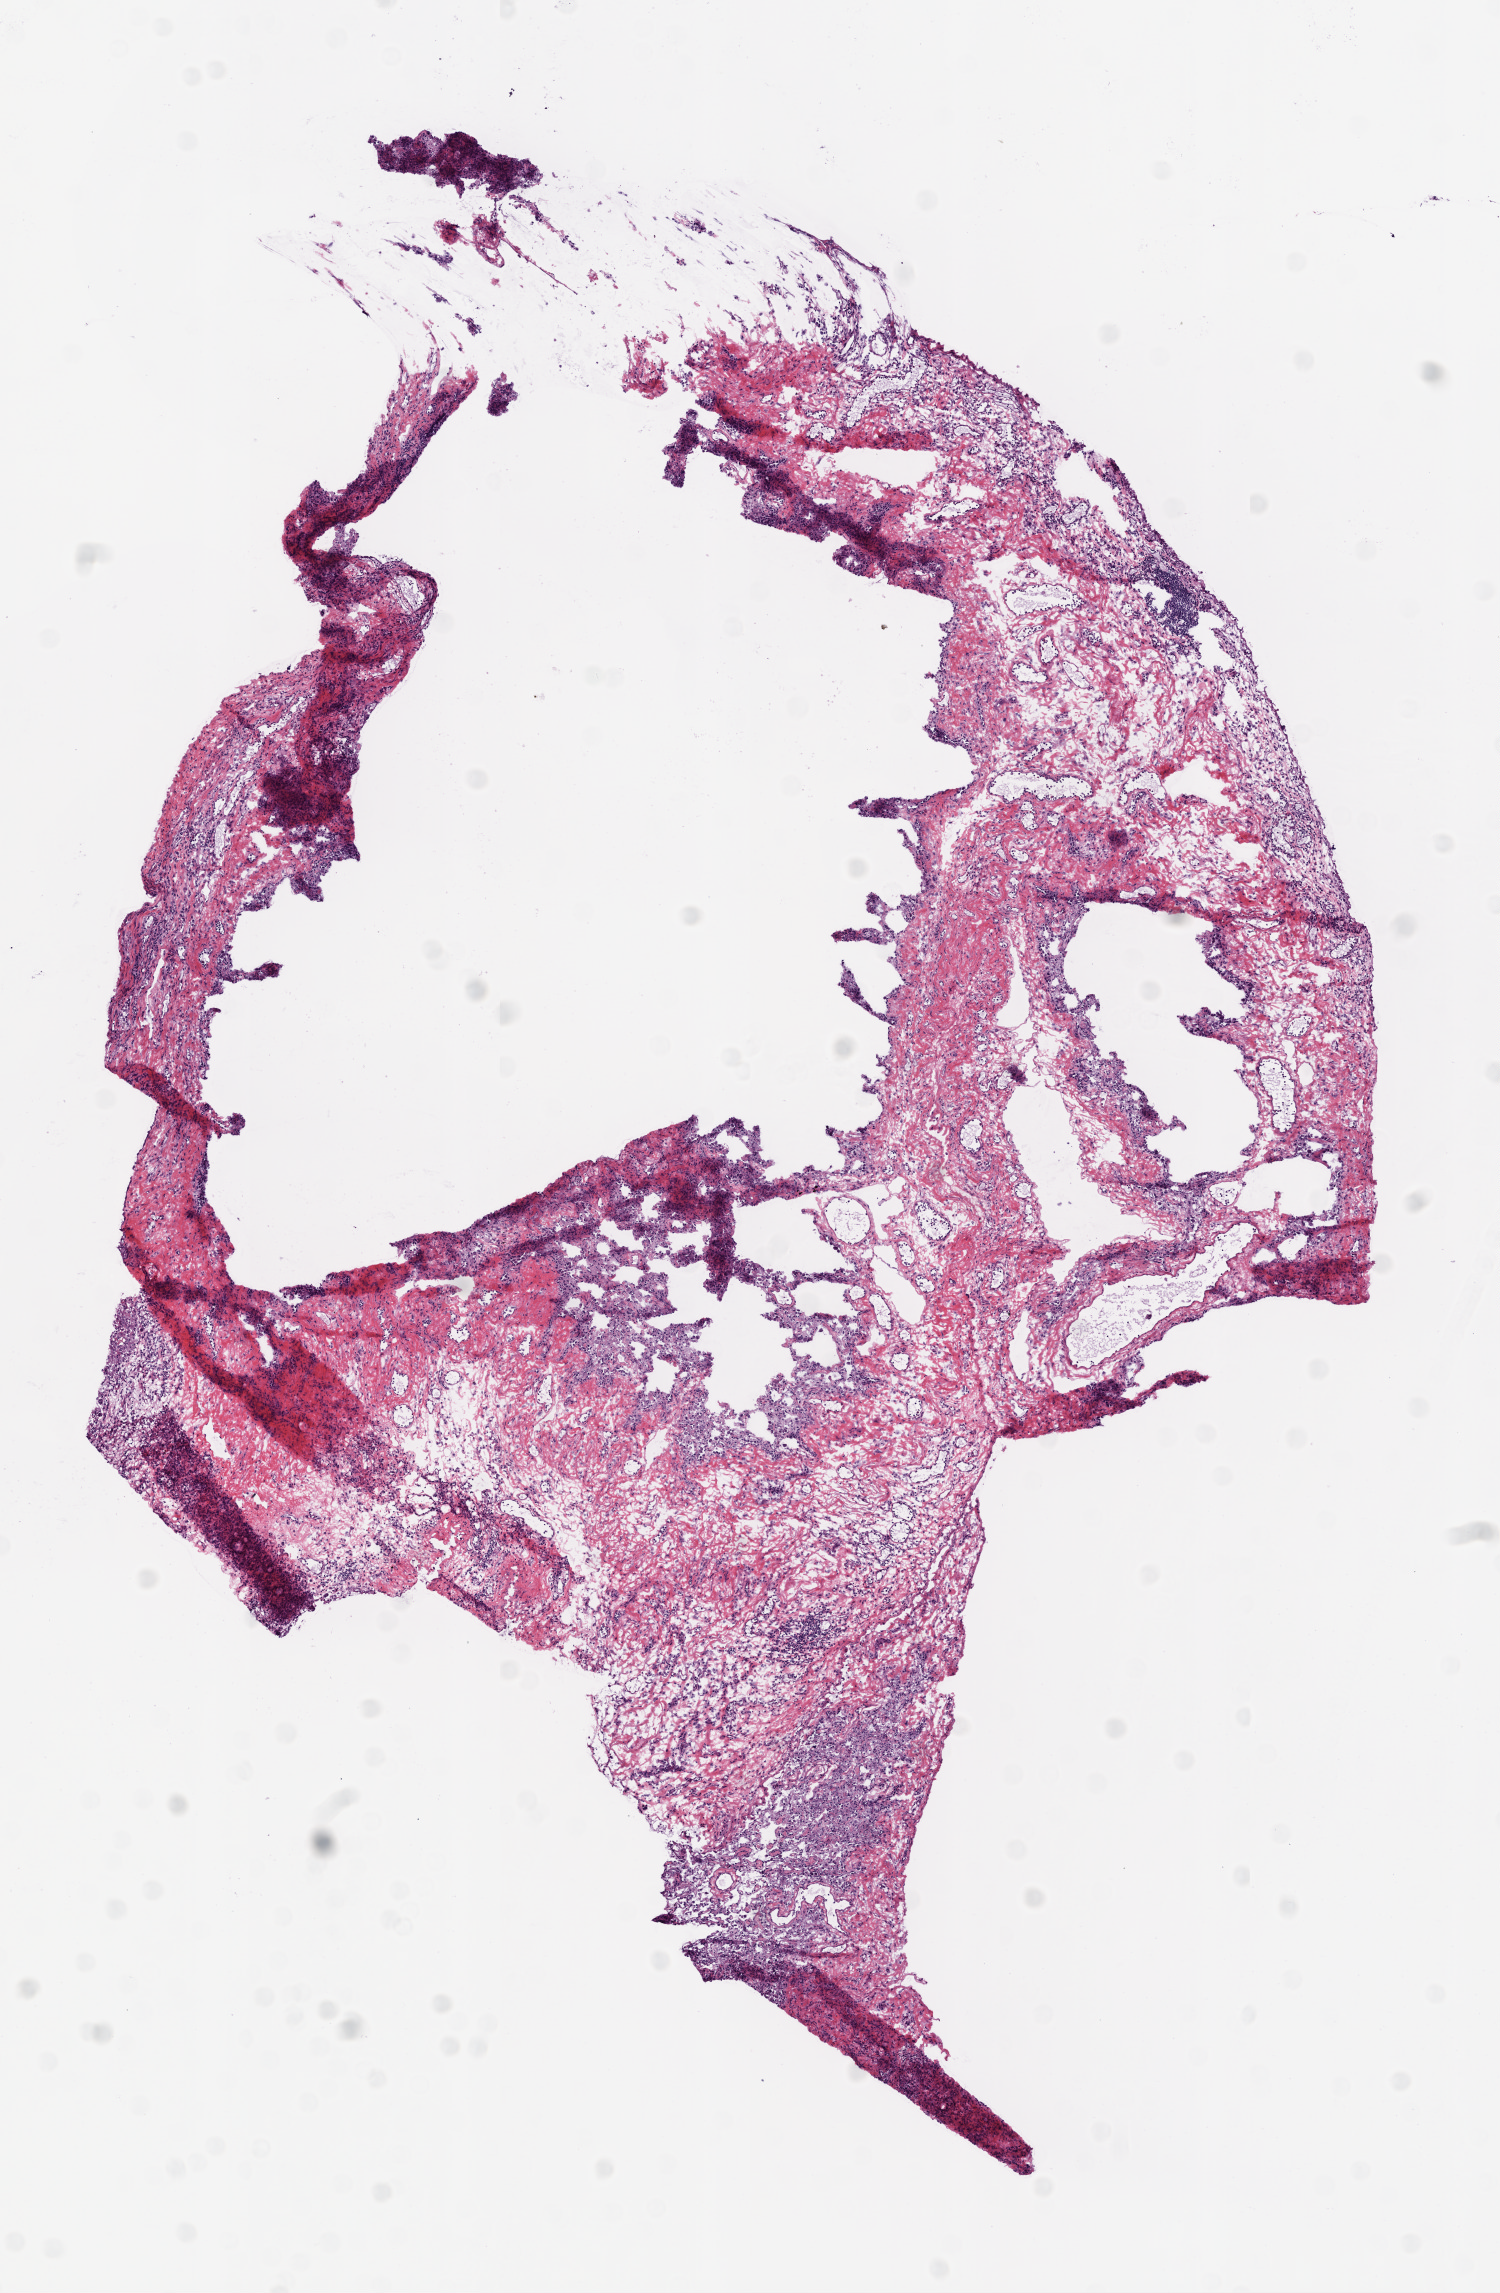
Whole-slide histology image, Hematoxylin and eosin (H&E) stained, a low-resolution overview of the entire scanned area, about 6.0 x 9.2 mm (from a 20x scan), frozen section from the top of the tissue portion, solid tissue normal (non-tumour tissue) sample from the lung. Patient: male, age at initial diagnosis 56 years.
This section: solid tissue normal (non-tumour) sample from the same patient. Patient diagnosis: Squamous cell carcinoma, NOS (lower lobe, lung).